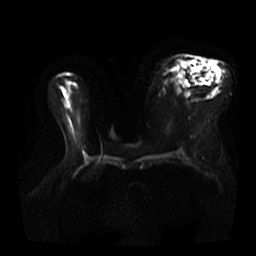
Breast MRI, one axial slice. Slice 20 of 40 in the series (ordered by position). Diffusion-weighted series; image 2 of 4 stored at this slice position (different b-values; order by instance number). 3 T. 5 mm slice thickness. 256 × 256 image matrix, field of view 360 × 360 mm. Female patient.
Annotated regions visible in this slice (expert manual segmentation):
- tumour on diffusion-weighted imaging: bounding box [x1, y1, x2, y2] px = [203, 68, 206, 72]